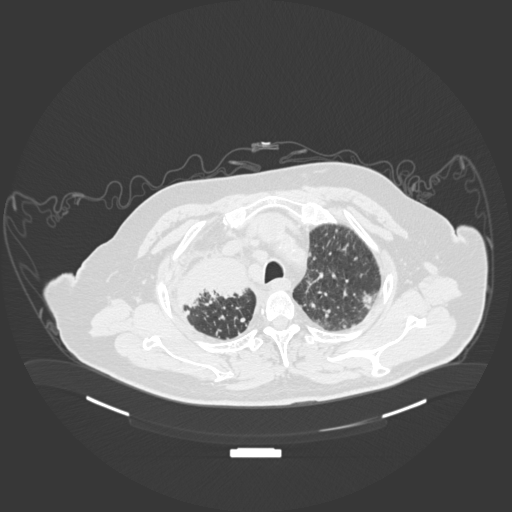
Chest CT, one axial slice. Slice 154 of 201 in the series (ordered by position). Reconstruction kernel B30f. Lung window (W 1500 / L -600 HU). 512 × 512 image matrix. Patient: male, 69 years. Case-level facts recorded for this patient, not image findings: clinical TNM (as recorded): T4 N3 M1.
Structures marked on this image (rectangle marked by the reading radiologist):
- lung tumour (recorded histology: adenocarcinoma): bounding box [x1, y1, x2, y2] px = [172, 250, 263, 315]